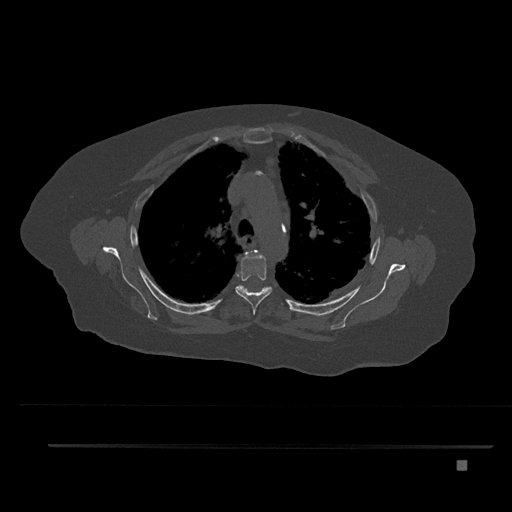
CT including the spine, one axial slice; slice 599 of 797 in the series (ordered by position); bone window (W 1800 / L 400 HU); 0.5 mm slice thickness; 512 × 512 image matrix. Patient: female, 76 years. From the clinical record (not read from this slice): primary cancer: lung; vertebrae with lytic lesions (as recorded): T11, L3.
Outlined on this slice (semi-automatically segmented with operator editing):
- T3 vertebra: bounding box <244,250,259,258> (left, top, right, bottom; pixels)
- T4 vertebra: <235,250,272,315>
- T5 vertebra: <237,284,271,294>